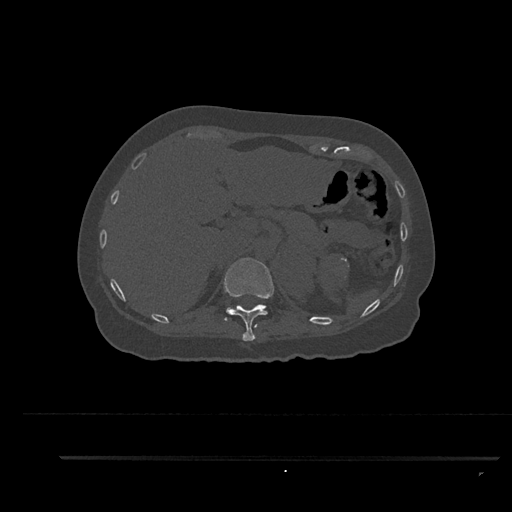
CT including the spine, one axial slice; position 306 of 797 along the scan axis; reconstruction kernel Br40s/3; 120 kVp; bone window (W 1800 / L 400 HU); 0.5 mm slice thickness; 512 × 512 image matrix. Female patient, age 44 years. From the clinical record (not read from this slice): primary cancer: renal; vertebrae with lytic lesions (as recorded): L1.
Structures marked on this image (semi-automatically segmented with operator editing):
- T11 vertebra: bounding box [x1, y1, x2, y2] px = [224, 258, 274, 341]
- T12 vertebra: [224, 304, 266, 321]